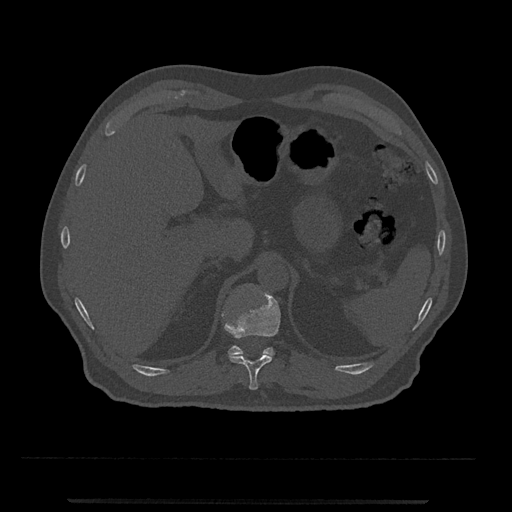
CT including the spine, one axial slice. Position 443 of 797 along the scan axis. 120 kVp. Bone window (W 1800 / L 400 HU). 512 × 512 image matrix, field of view 419 × 419 mm. Patient: male, 63 years. Case-level facts recorded for this patient, not image findings: primary cancer: prostate.
Annotated regions visible in this slice (semi-automatically segmented with operator editing):
- T11 vertebra: bounding box [x1, y1, x2, y2] px = [222, 292, 281, 390]
- T12 vertebra: [228, 322, 275, 356]